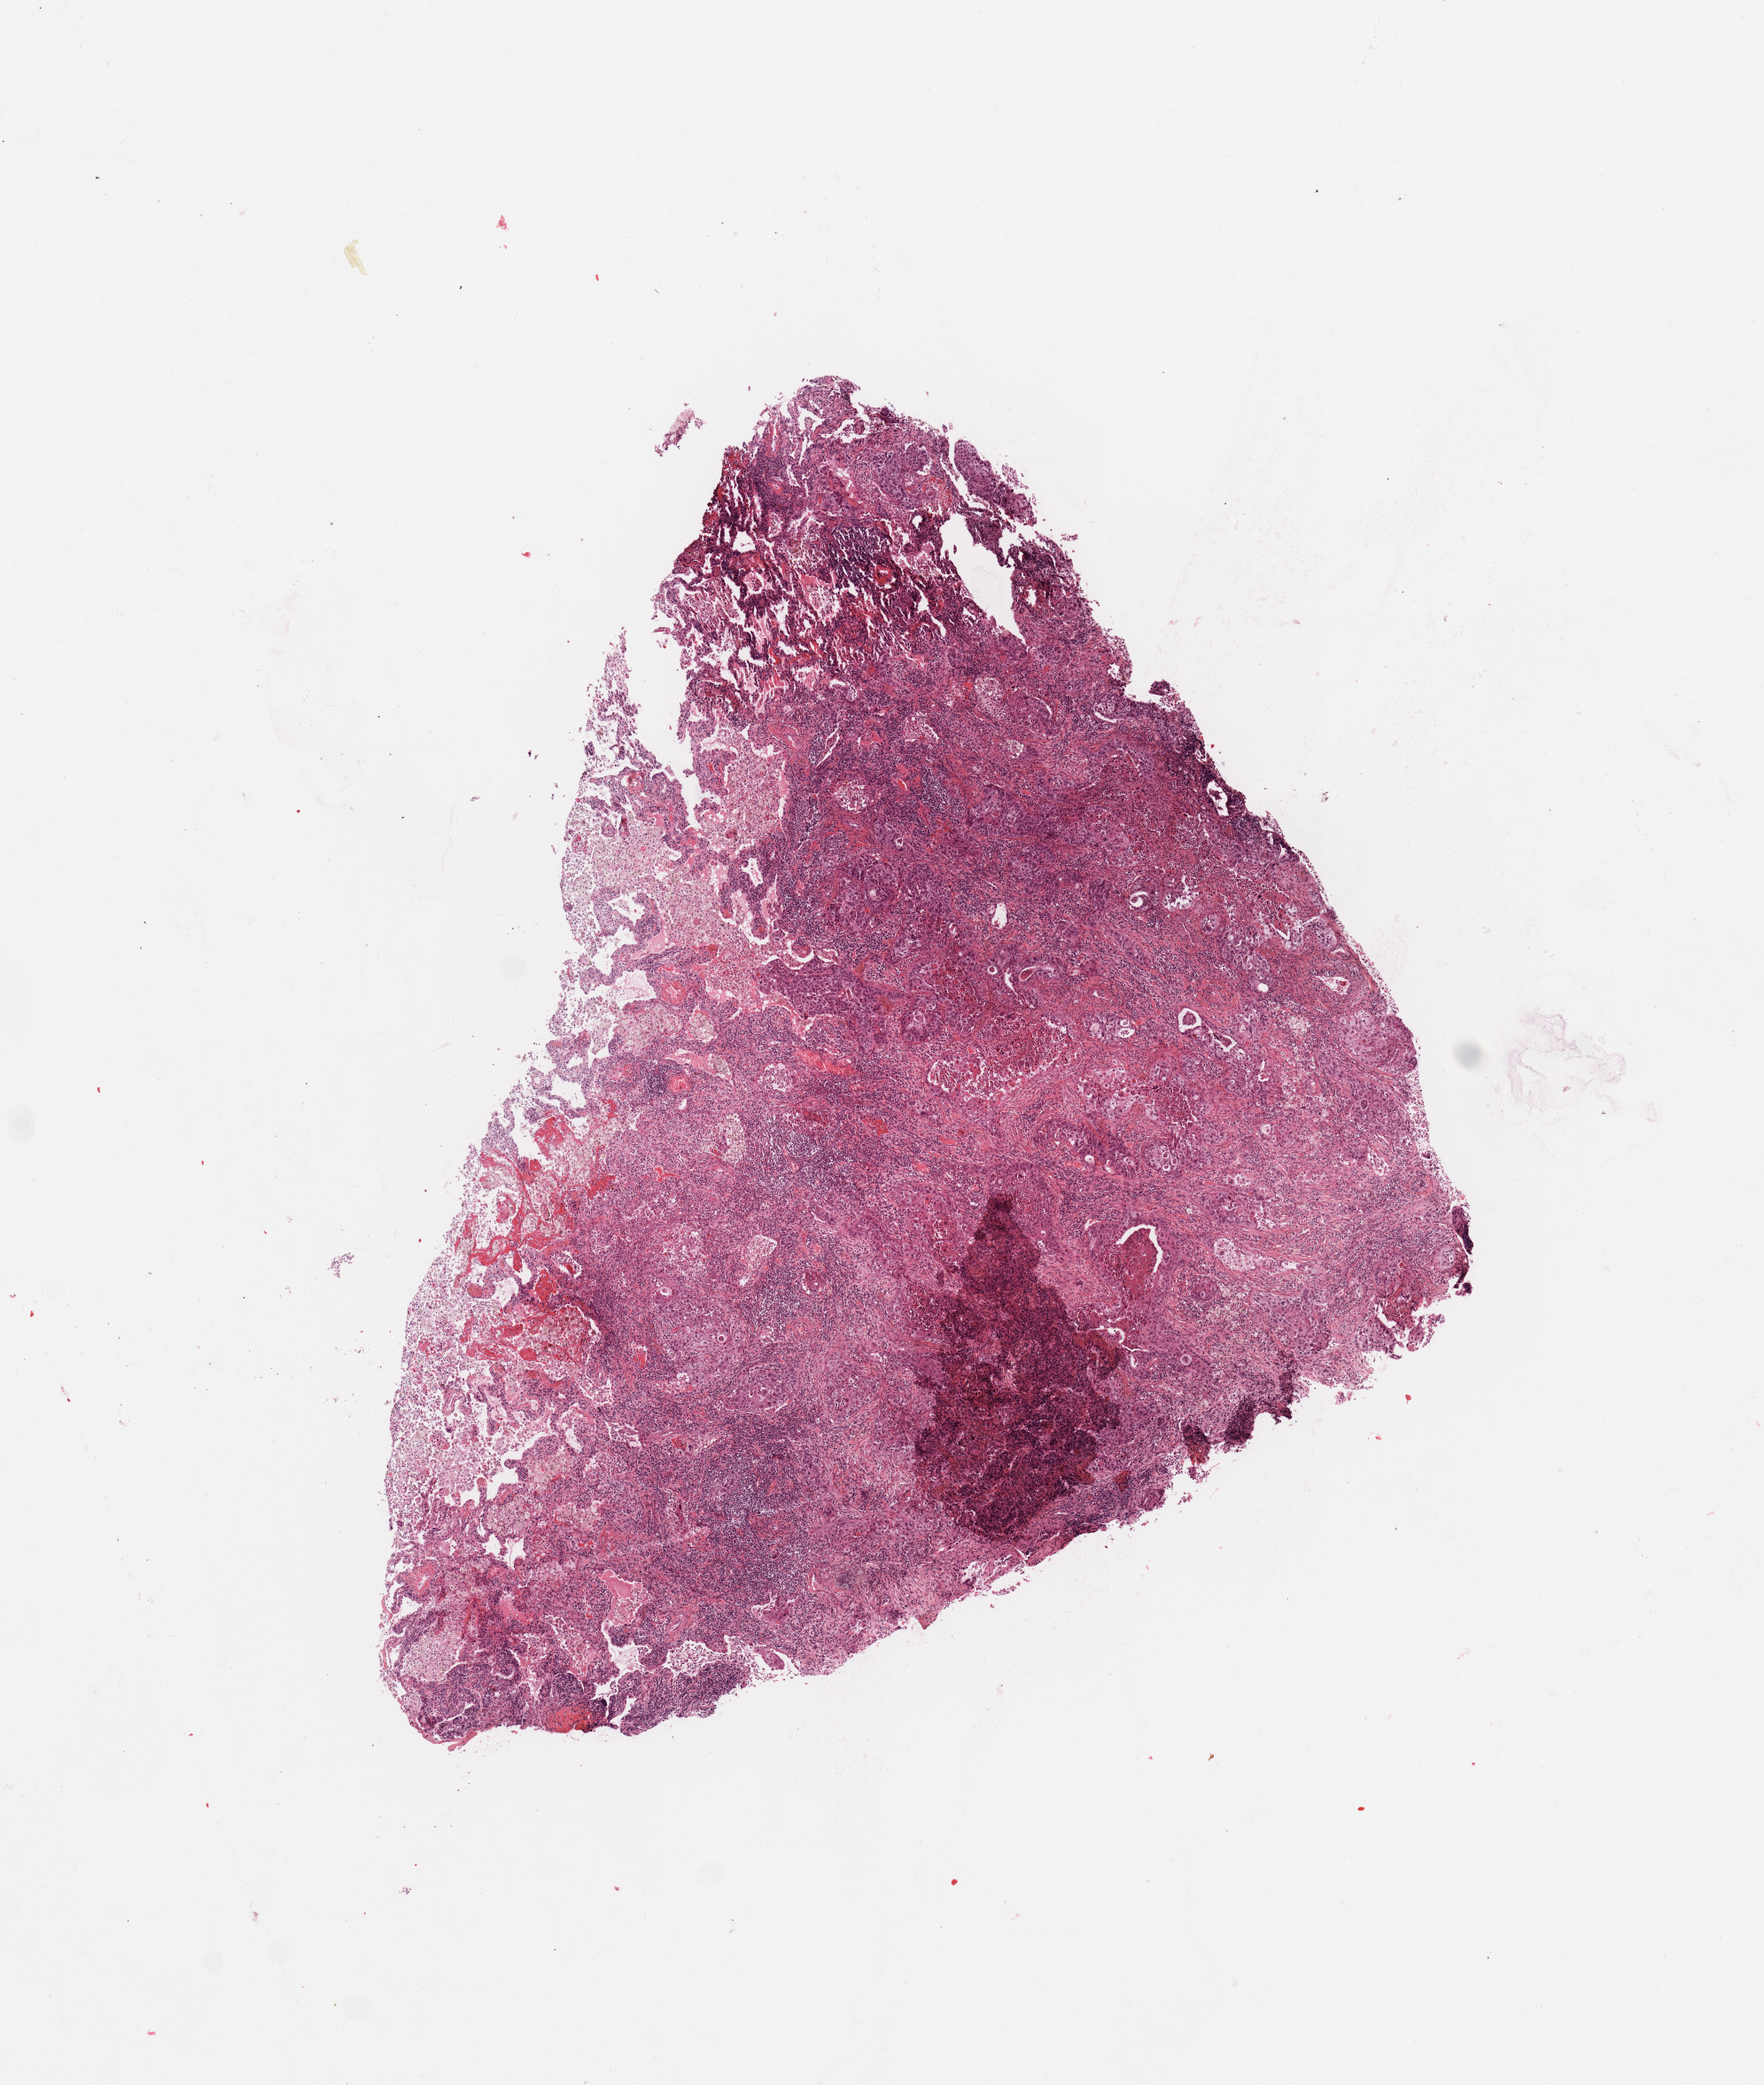
Whole-slide histology image, H&E, low-resolution overview of the scanned area, about 7.9 x 9.3 mm (slide scanned at 20x), tumour tissue sample, sampled site: lung. 63-year-old male patient. Histologic grade: G2 (moderately differentiated). Slide review estimates, as recorded: tumour nuclei 70%, necrosis 5%.
• diagnosis: Squamous cell carcinoma, NOS
• primary tumour site (as recorded): right lower lobe
• AJCC pathologic stage: IIIA